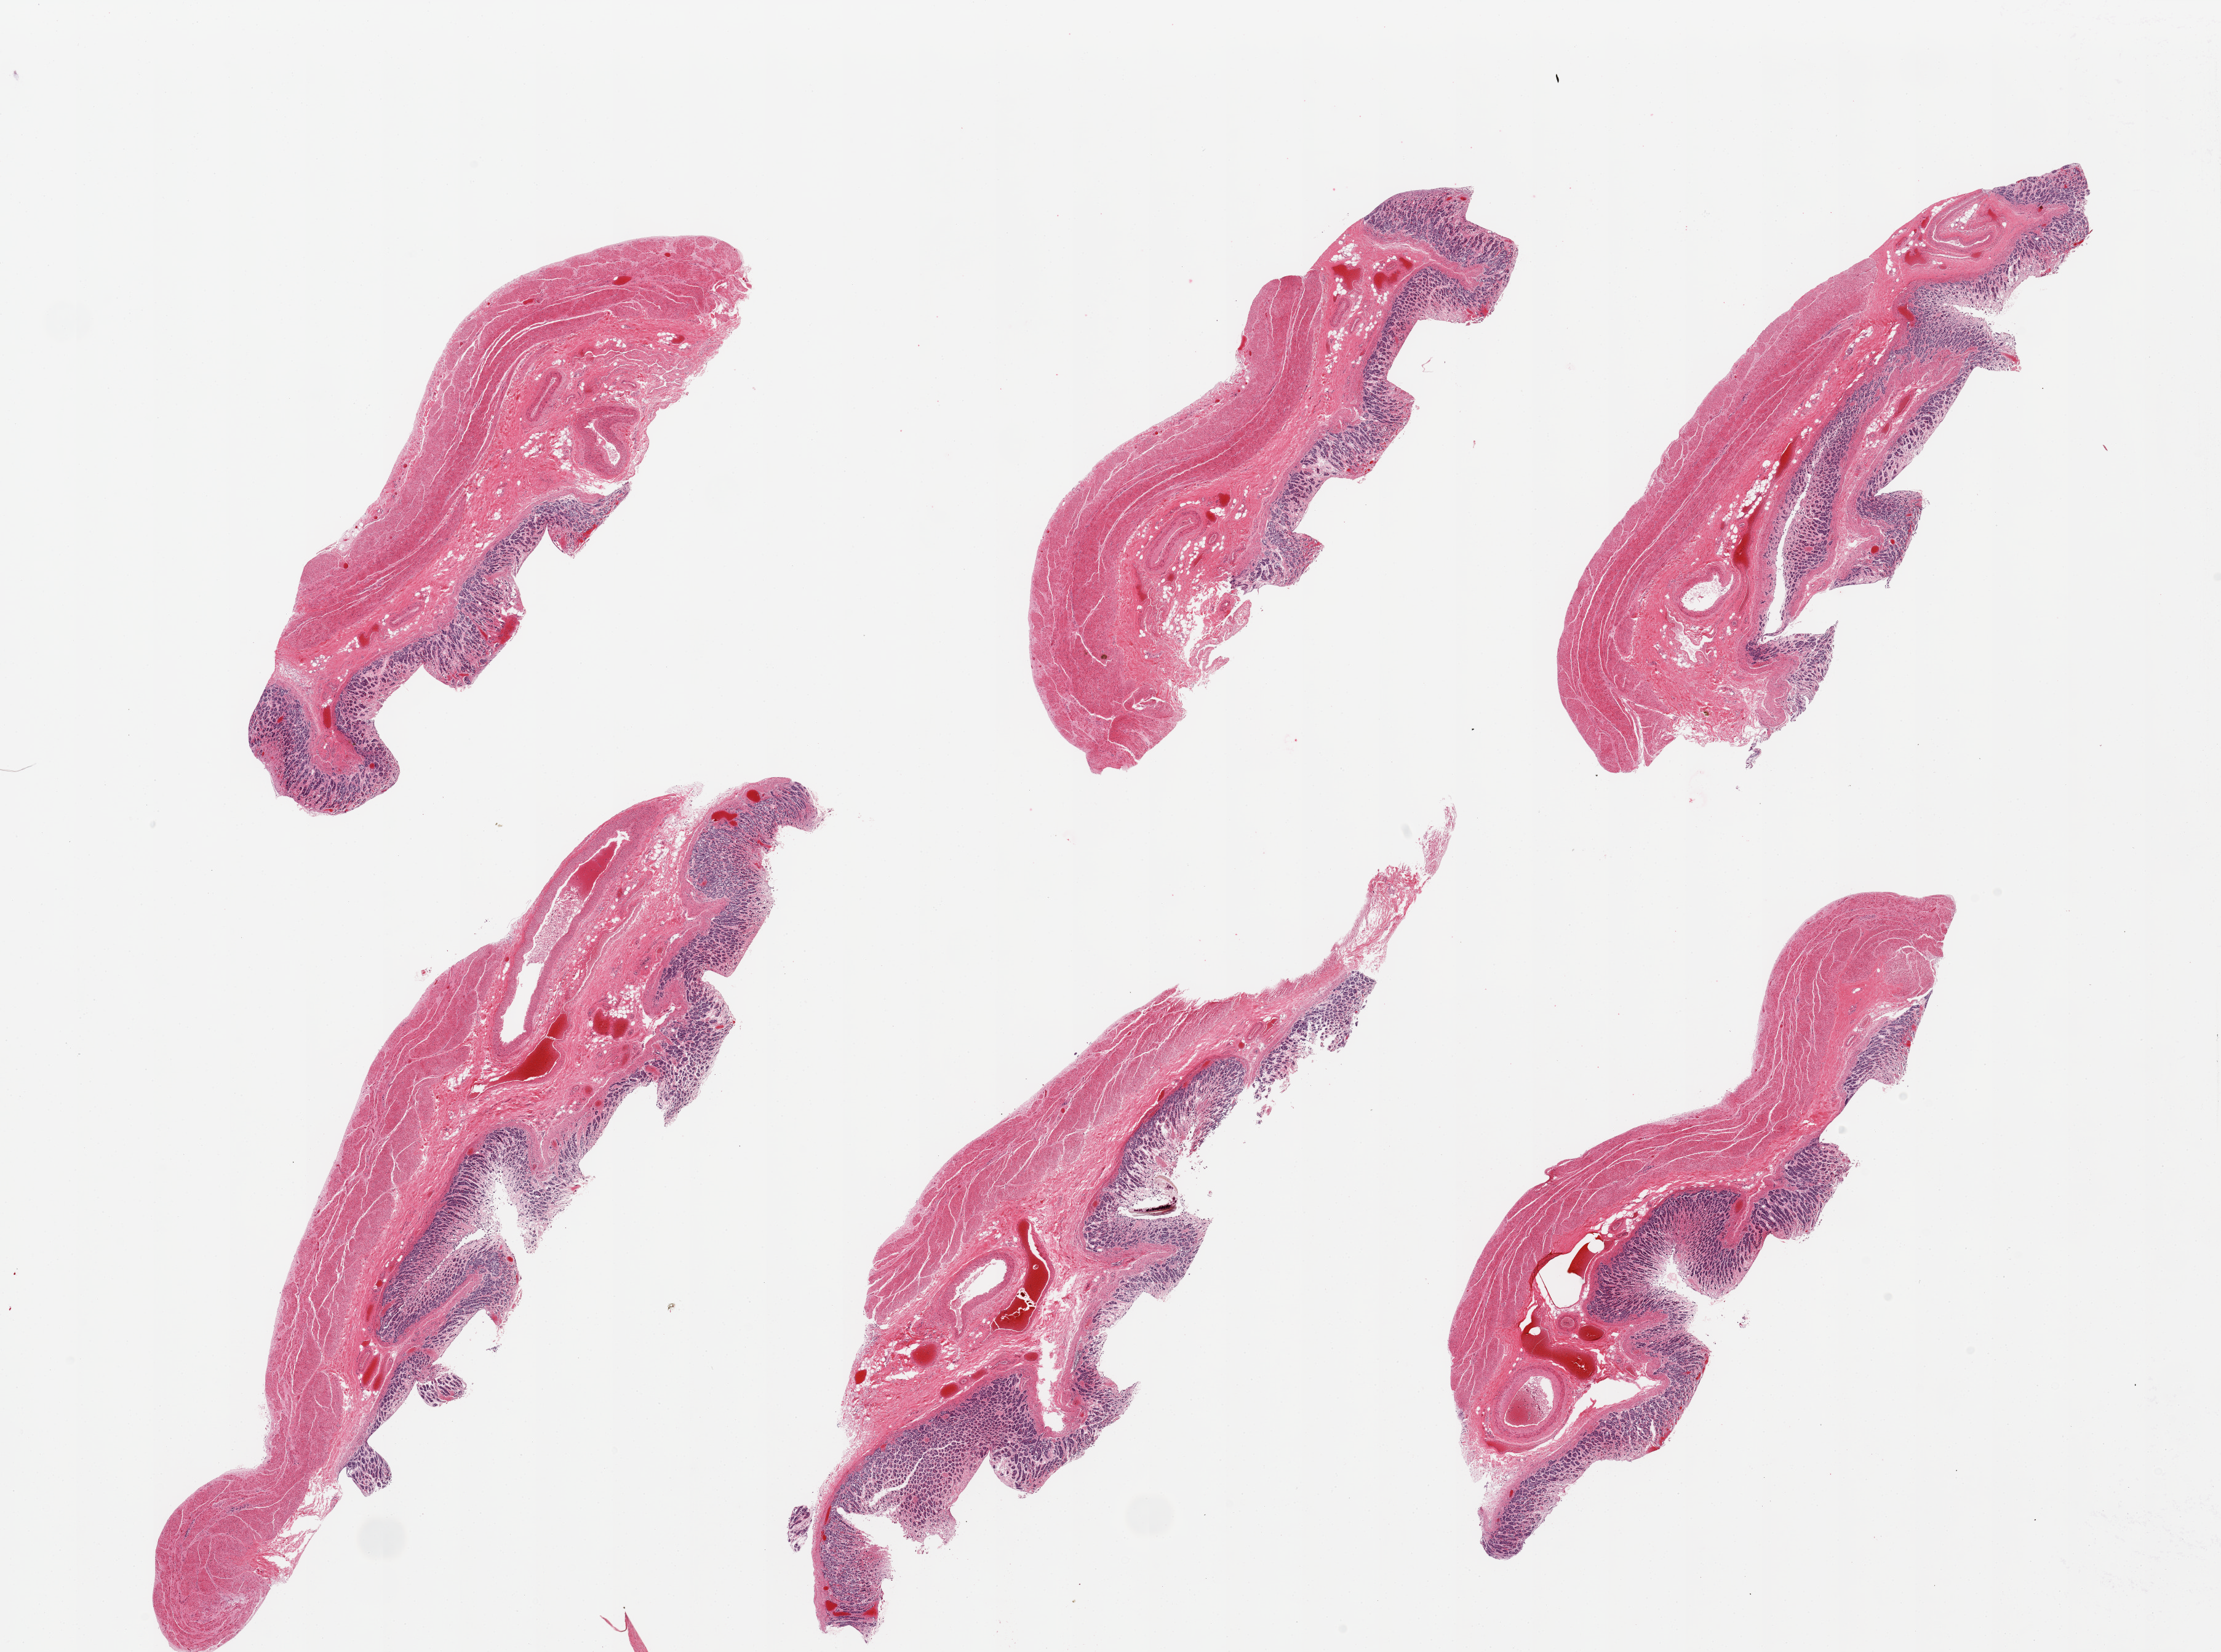
H&E whole-slide image, shown as a low-resolution overview of the whole scanned area (about 28.5 x 21.2 mm). PAXgene-fixed, paraffin-embedded tissue. Sampled site (target tissue): stomach. Tissue donor sample. Donor: male.
Reviewer comment on this tissue sample: 6 pieces; full thickness sections with moderately to severely autolyzed mucosa, foveolar cells sloughed.